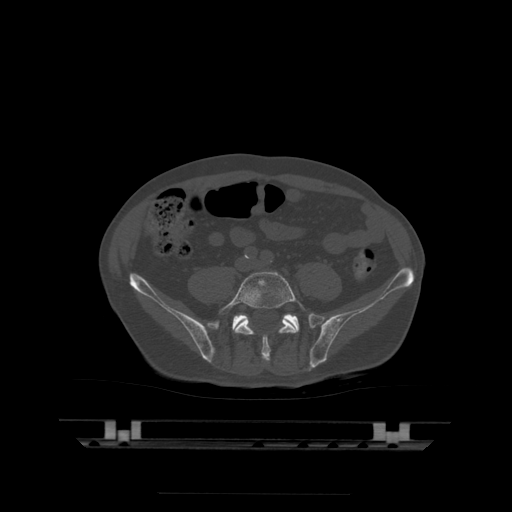
CT including the spine, one axial slice. Position 69 of 522 along the scan axis. Bone window (W 1800 / L 400 HU). 512 × 512 image matrix. Patient age 68 years. From the clinical record (not read from this slice): primary cancer: urothelial.
Annotated regions visible in this slice (semi-automatically segmented with operator editing):
- L5 vertebra: bounding box <219,271,312,362> (left, top, right, bottom; pixels)